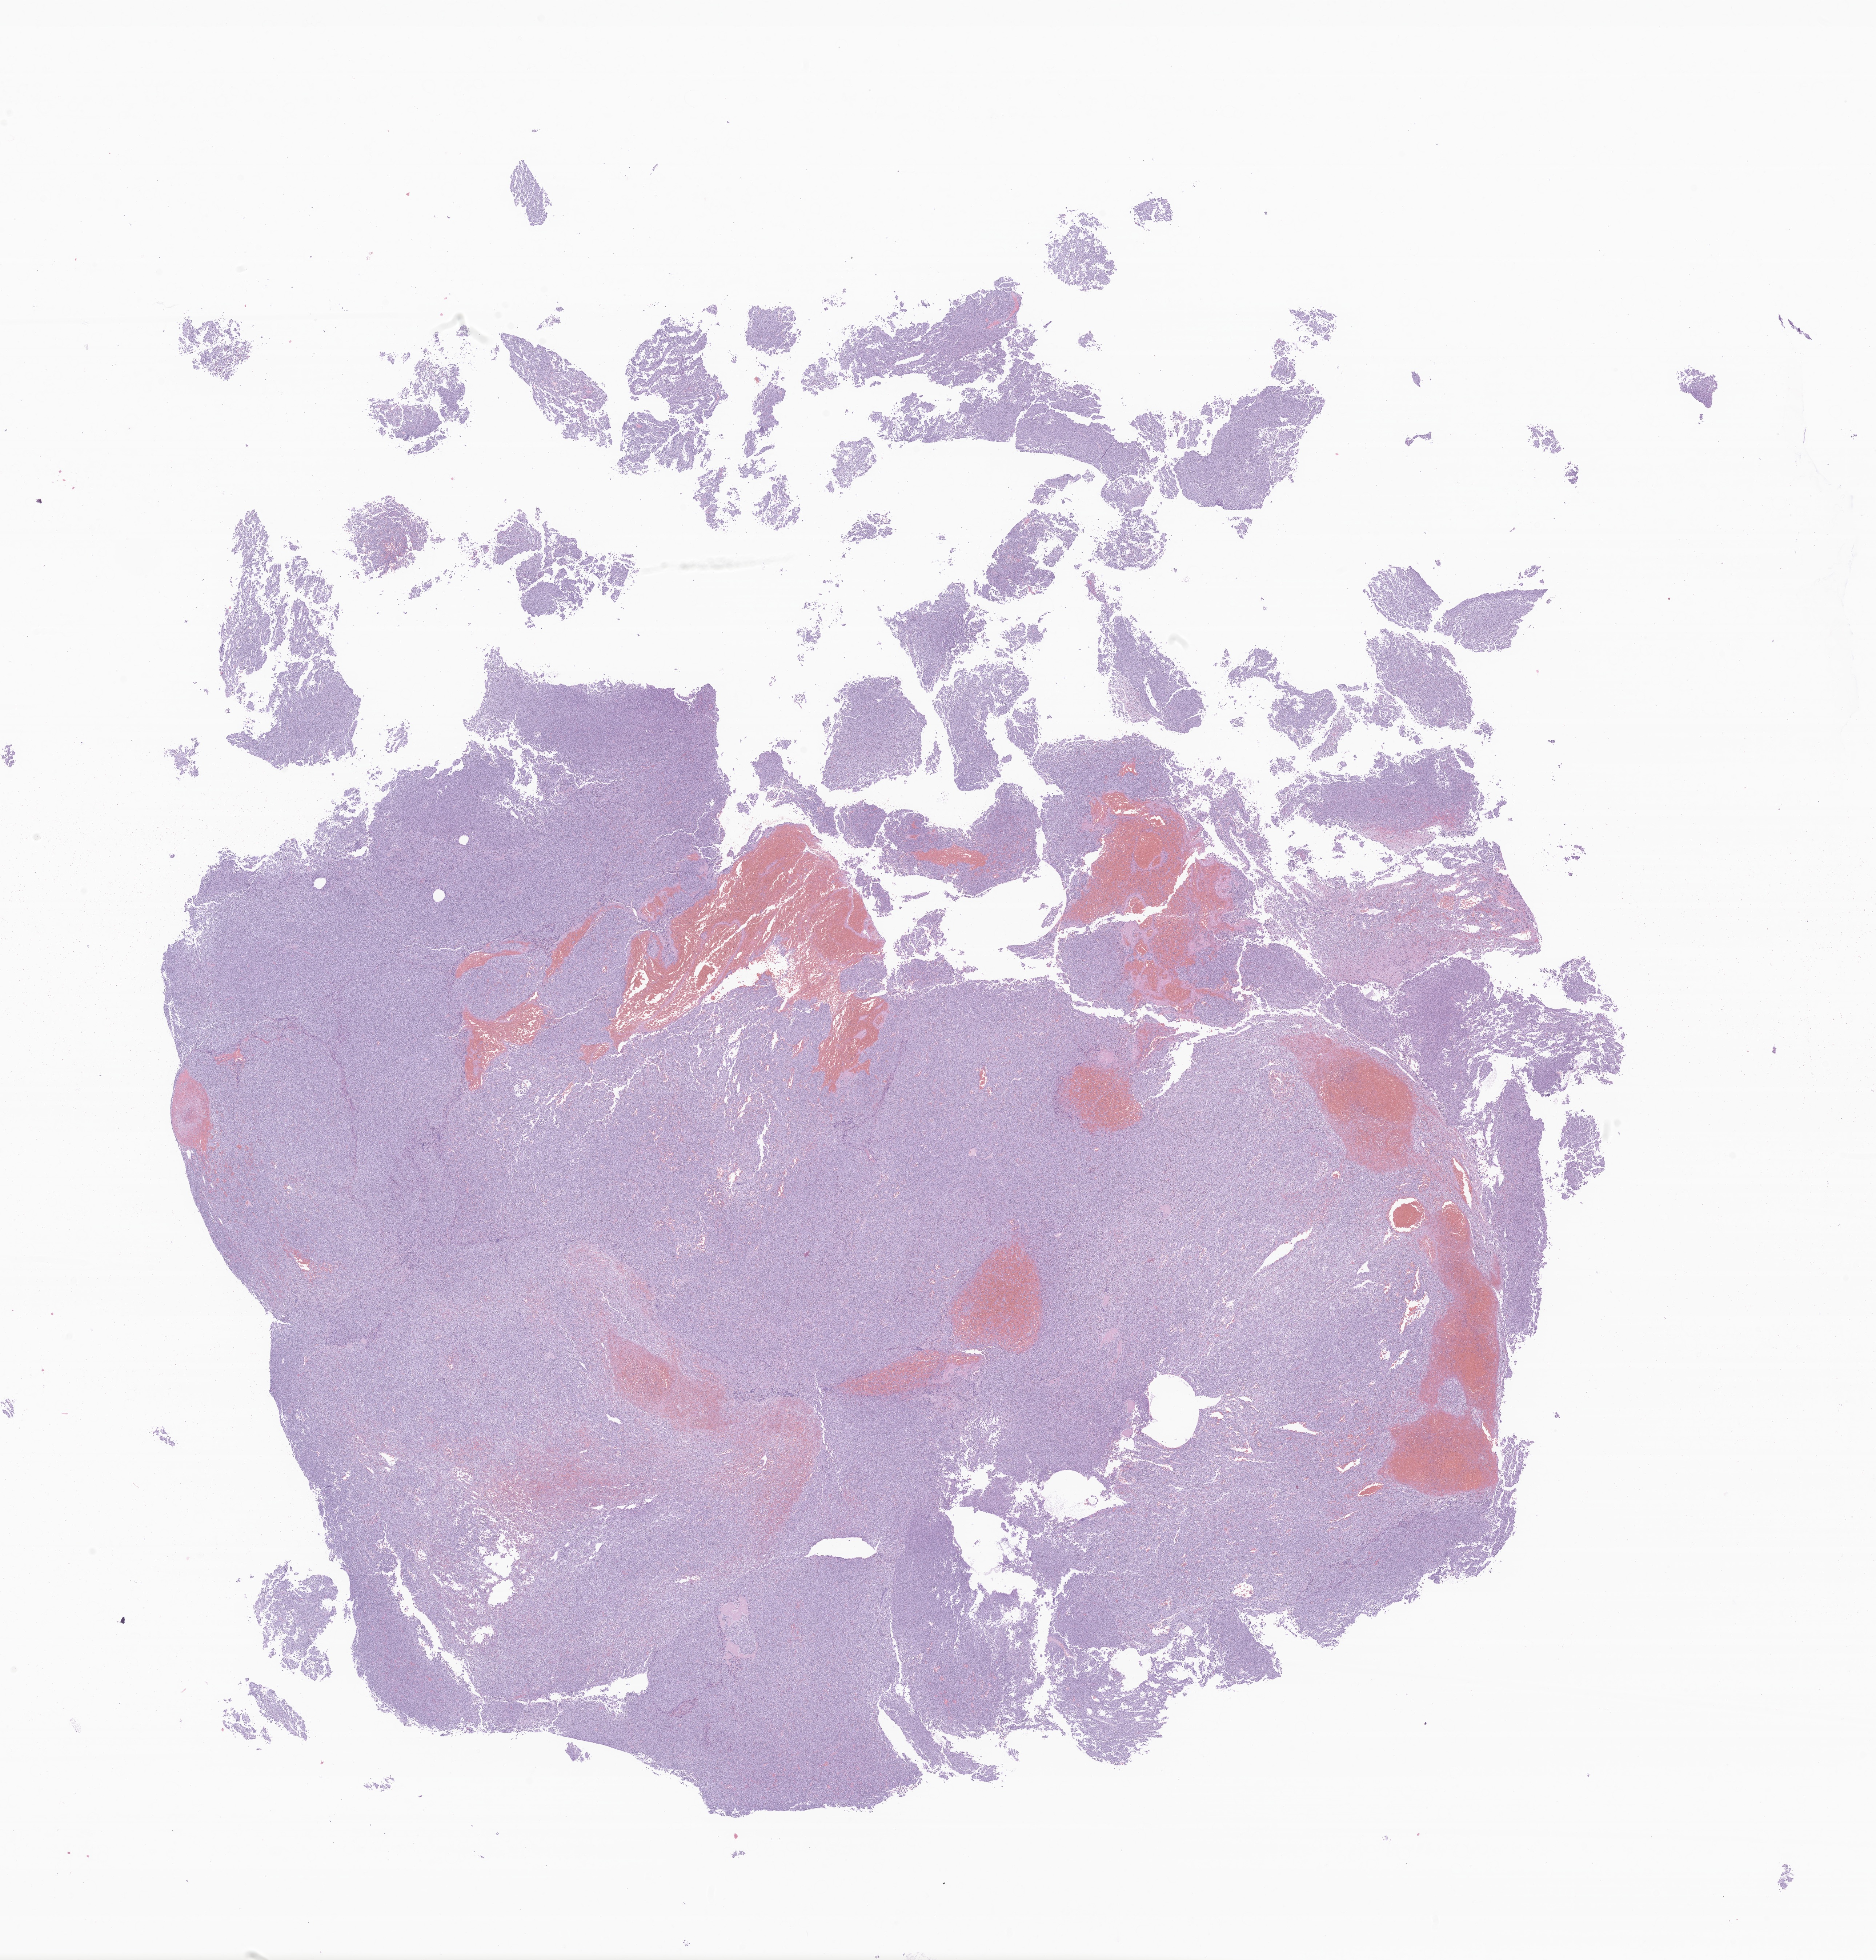
Whole-slide image, H&E stain of tumor tissue from the adrenal gland — shown as a low-resolution overview of the whole scanned area (about 21.8 x 22.7 mm), formalin-fixed paraffin-embedded section. Patient: female, age 226 days.
Diagnosis (ICD-O-3 morphology term): Neoplasm, malignant.